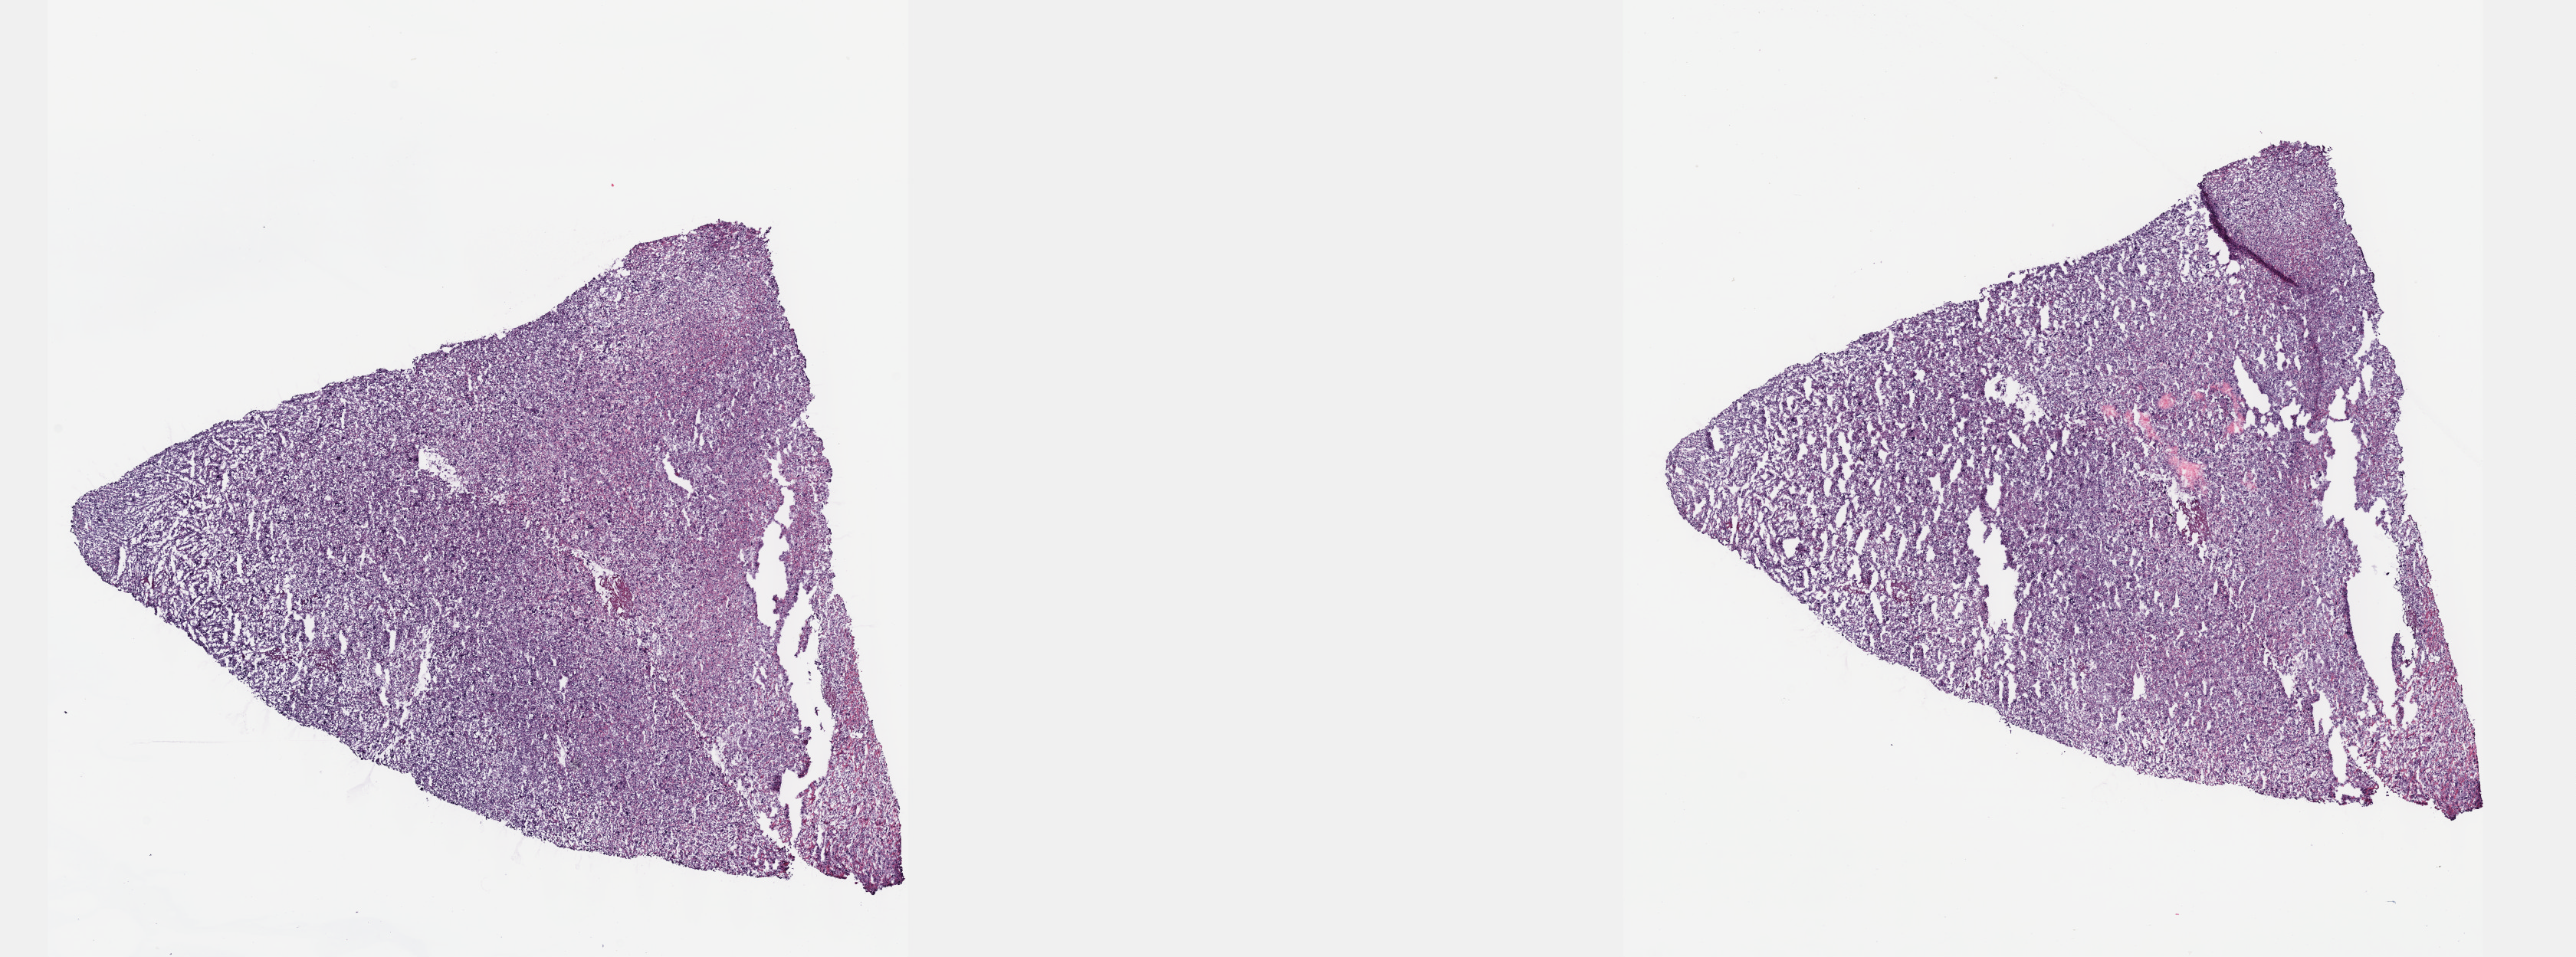
Digitized H&E tissue section (whole slide) — whole scanned area (about 27.2 x 10.1 mm) shown as a low-resolution overview. Frozen section from the top of the tissue portion. Primary tumour sample from the connective, subcutaneous and other soft tissues. Female, age 68 years at initial diagnosis. Slide review estimates, as recorded: tumour cells 80%, tumour nuclei 80%, normal cells 0%, stromal cells 18%, necrosis 2%. Inflammatory infiltration, as recorded: lymphocyte infiltration 2%, monocyte infiltration 1%, neutrophil infiltration 2%.
* pathologic diagnosis: Undifferentiated sarcoma (connective, subcutaneous and other soft tissues of lower limb and hip)